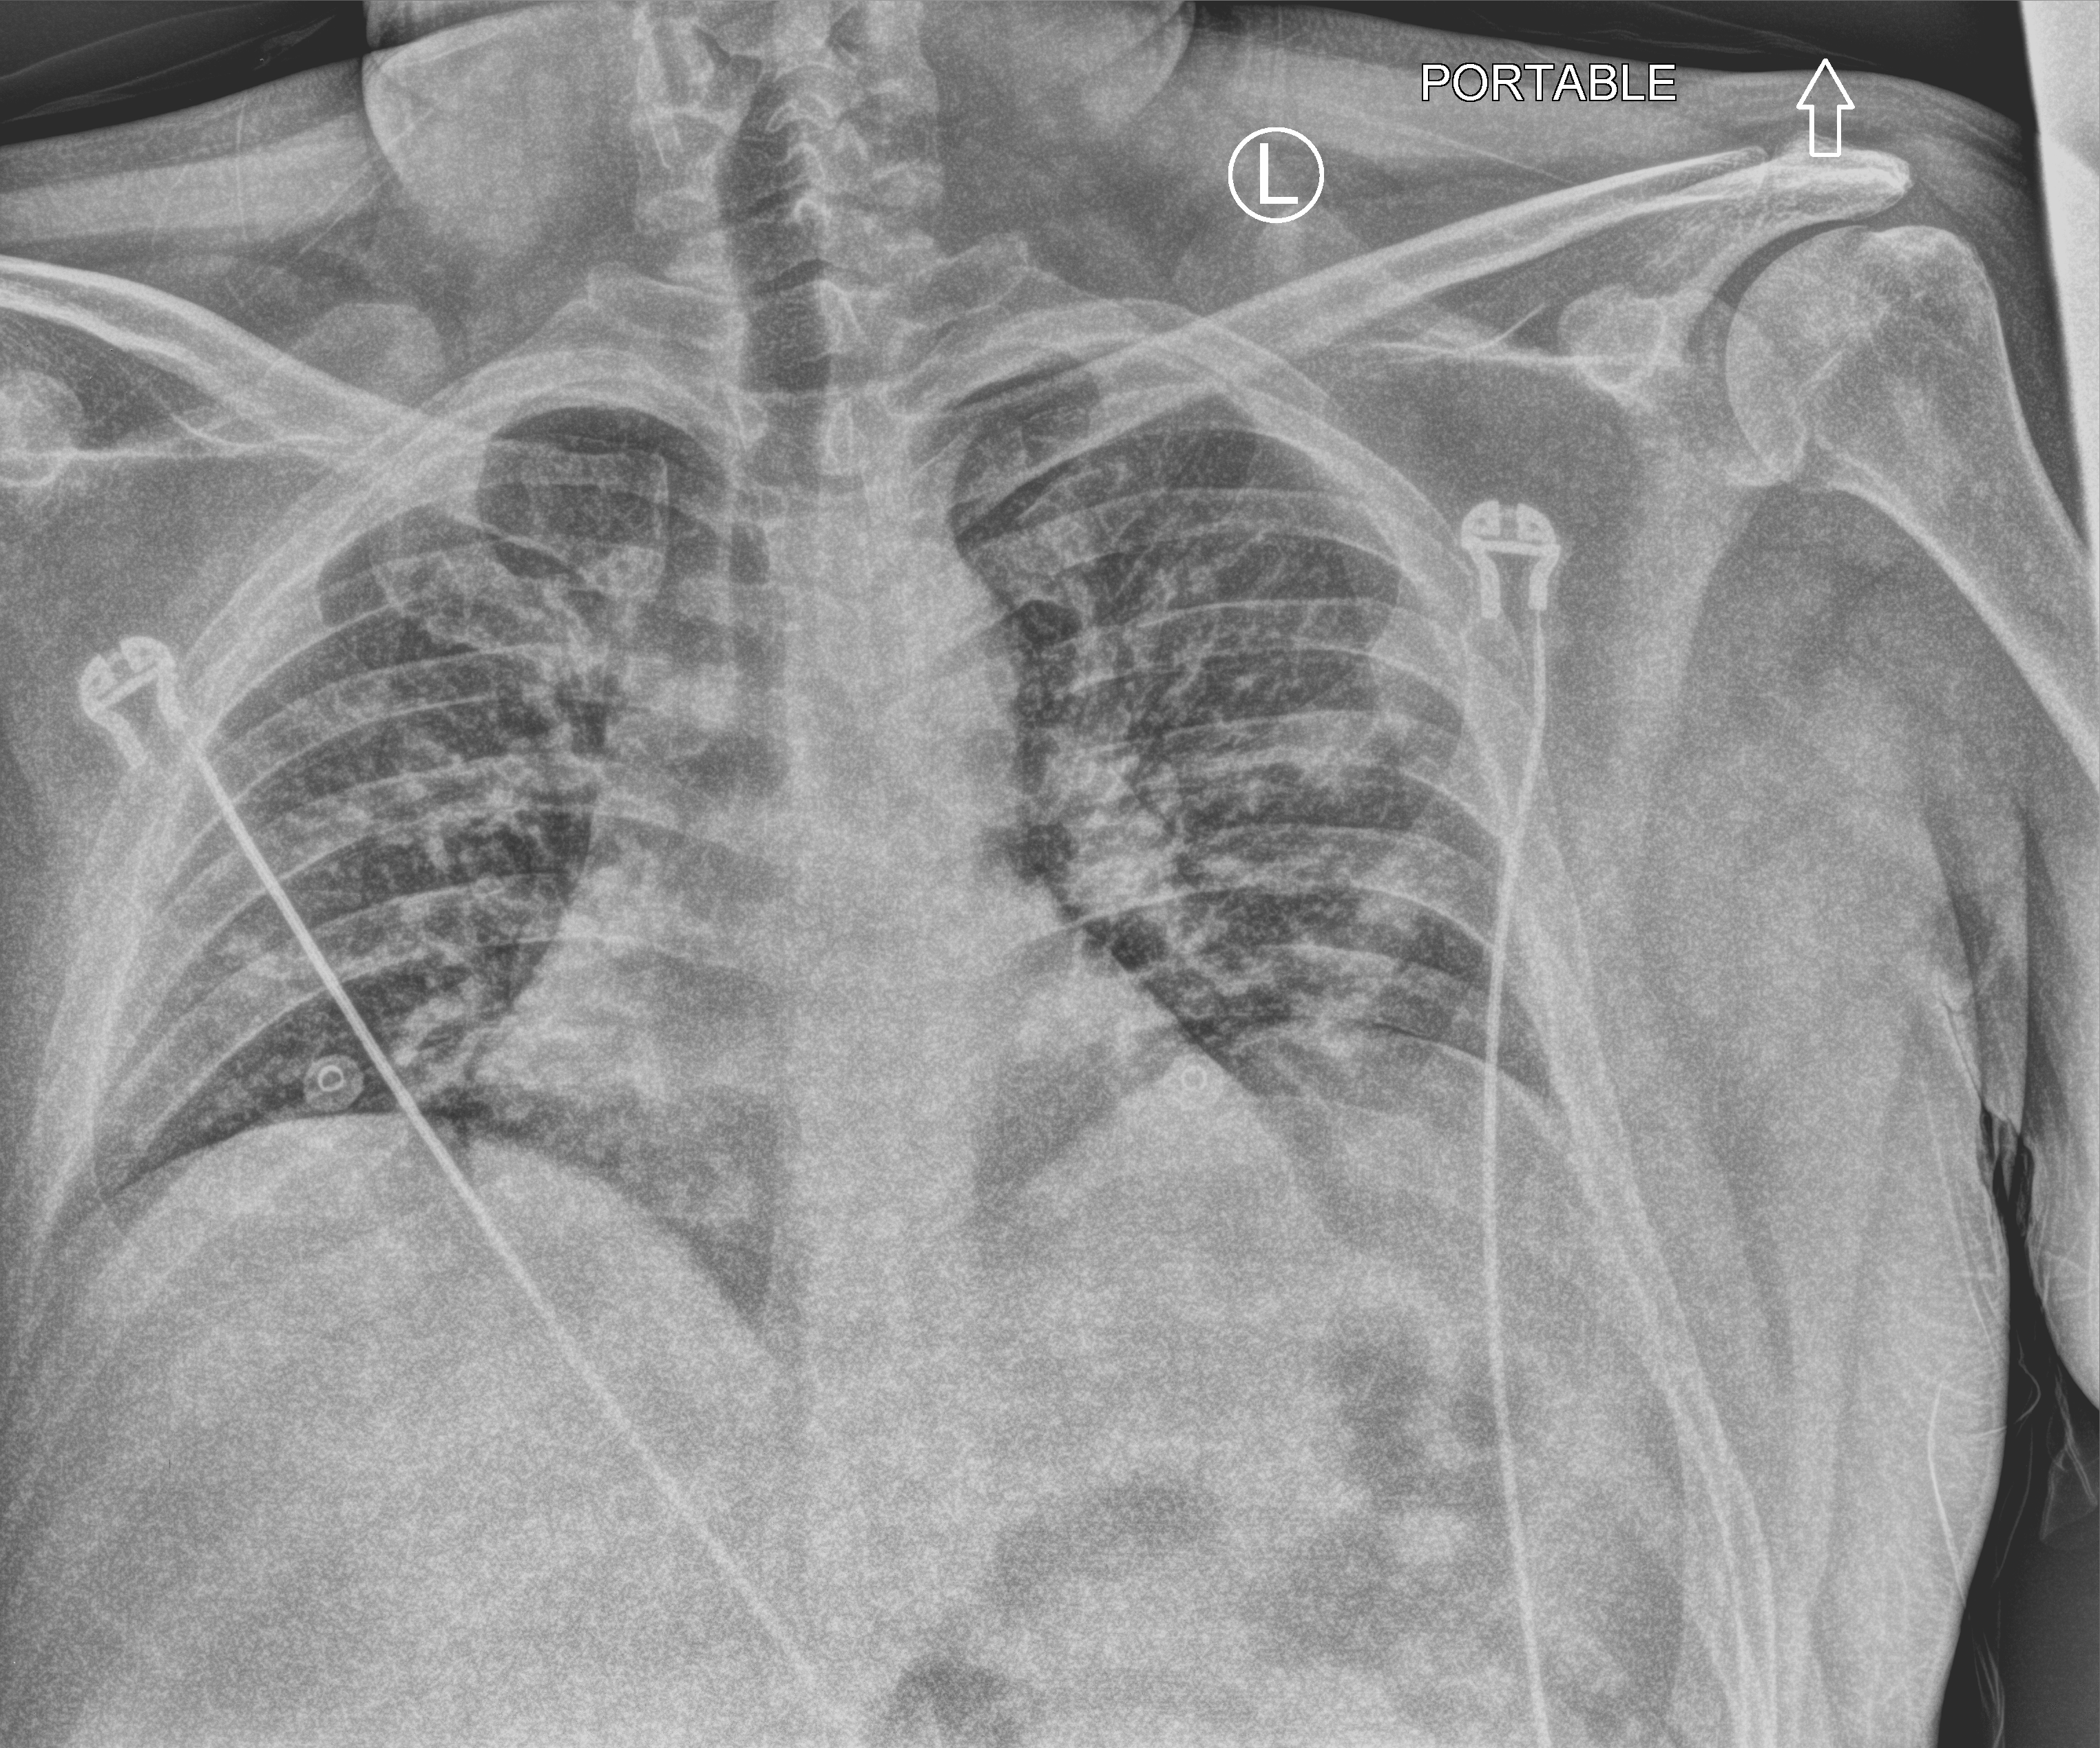
Chest X-ray (portable); anteroposterior (AP) projection. Patient hospitalised with COVID-19; male, aged 18–59 years.
From the hospital-stay record, not from the radiograph (when in the stay this image was taken is not recorded): admitted to intensive care during this hospital stay: no; mechanically ventilated during this hospital stay: no; length of hospital stay: 1 day.